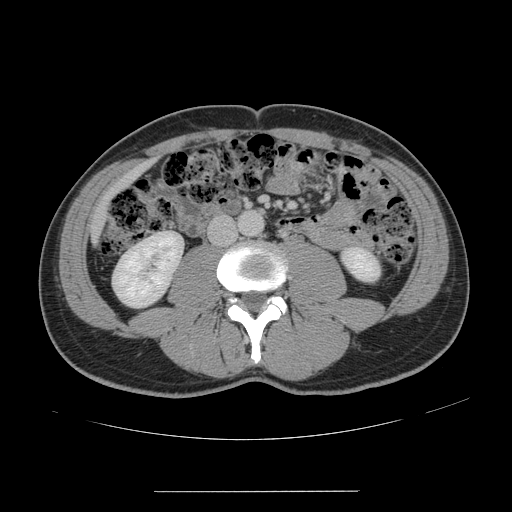
Contrast-enhanced abdominal CT, one axial slice. Slice 28 of 178 in the series (ordered by position). 120 kVp. Soft-tissue window (W 400 / L 40 HU). 2.5 mm slice thickness. 512 × 512 image matrix. Male patient, age 53 years. Case-level facts recorded for this patient, not image findings: diagnosis: colorectal cancer liver metastases, imaged before liver resection; multiple liver metastases: yes; largest metastasis: 2.4 cm; disease in both lobes: no.
Outlined on this slice (outlined manually by an expert reader):
- liver: bounding box (x1, y1, x2, y2) in pixels: (94, 164, 148, 237)